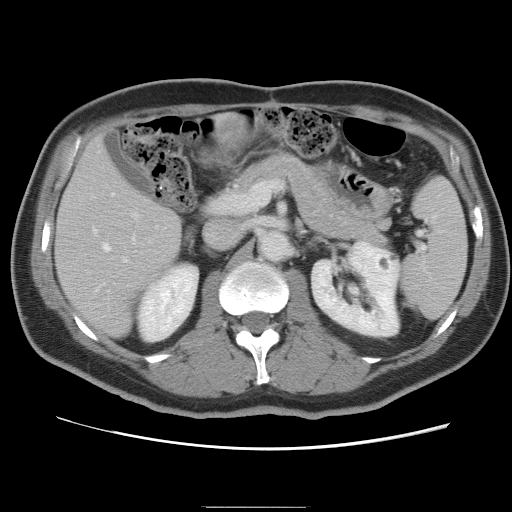
Contrast-enhanced abdominal CT, one axial slice. 120 kVp. Intravenous contrast given. Soft-tissue window (W 400 / L 40 HU). 5 mm slice thickness. 512 × 512 image matrix. Male patient, age 63 years. Case-level facts recorded for this patient, not image findings: diagnosis: colorectal cancer liver metastases, imaged before liver resection; multiple liver metastases: no; largest metastasis: 9 cm; disease in both lobes: no.
Structures marked on this image (expert manual segmentation):
- hepatic veins: box from (x=93, y=193) to (x=134, y=251) px
- liver: (x=57, y=115)–(x=253, y=337)
- planned liver remnant (the part of the liver to remain after resection): (x=56, y=146)–(x=182, y=337)
- portal vein (with intrahepatic branches): (x=108, y=212)–(x=140, y=292)
- liver metastasis: (x=219, y=119)–(x=245, y=134)